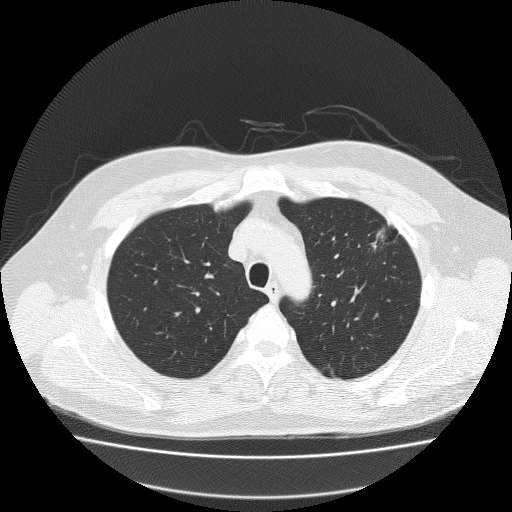
Chest CT (low-dose screening protocol), one axial image, first (baseline) screen, lung window (W 1500 / L -600 HU), 120 kVp, slice 46 of 204 in the series. Male participant, aged 62 years at enrolment.
- Expert-annotated lung lesion, bounding box (x1, y1, x2, y2) in pixels: (348, 216, 415, 267).
- Reader record for this screening exam (exam-level; its link to the box is not recorded): non-calcified nodule or mass ≥4 mm, left upper lobe, 18 × 8 mm, spiculated (stellate) margins, soft tissue attenuation.
- Official screen result: positive, change unspecified: nodule(s) >= 4 mm or enlarging nodule(s), mass(es), or other non-specific abnormalities suspicious for lung cancer.
- Later outcome: lung cancer diagnosed 49 days after this screen — bronchiolo-alveolar adenocarcinoma, NOS, left upper lobe, well differentiated (G1), stage IA (AJCC 6th edition), 25 mm at pathology.